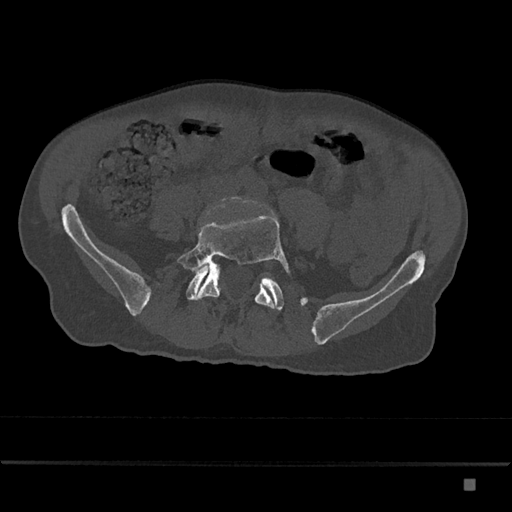
CT including the spine, one axial slice. Slice 273 of 797 in the series (ordered by position). Reconstruction kernel Br40s/3. 120 kVp. Bone window (W 1800 / L 400 HU). 0.5 mm slice thickness. 512 × 512 image matrix, field of view 390 × 390 mm. Male patient, age 72 years. Case-level facts recorded for this patient, not image findings: primary cancer: prostate.
Outlined on this slice (semi-automatic segmentation, software-assisted and operator-edited):
- L5 vertebra: bounding box (x1, y1, x2, y2) in pixels: (177, 205, 290, 309)